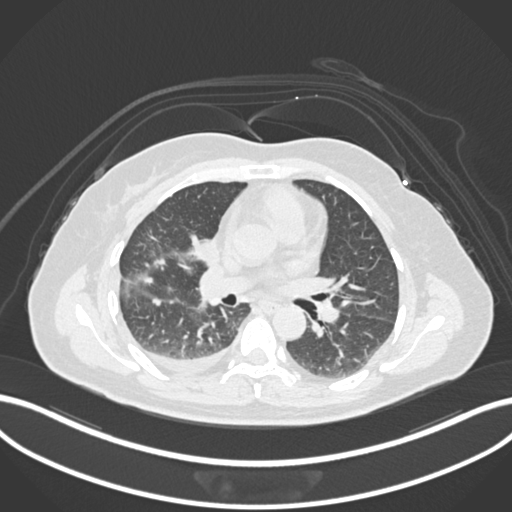
Chest CT, one axial slice; position 74 of 172 along the scan axis; reconstruction kernel B30f; 120 kVp; lung window (W 1500 / L -600 HU); 1 mm slice thickness; 512 × 512 image matrix, field of view 400 × 400 mm. Female patient, age 52 years. Case-level facts recorded for this patient, not image findings: clinical TNM (as recorded): T3 N1 M1.
Outlined on this slice (bounding box drawn by a radiologist):
- lung tumour (recorded histology: adenocarcinoma): bounding box <193,232,218,264> (left, top, right, bottom; pixels)